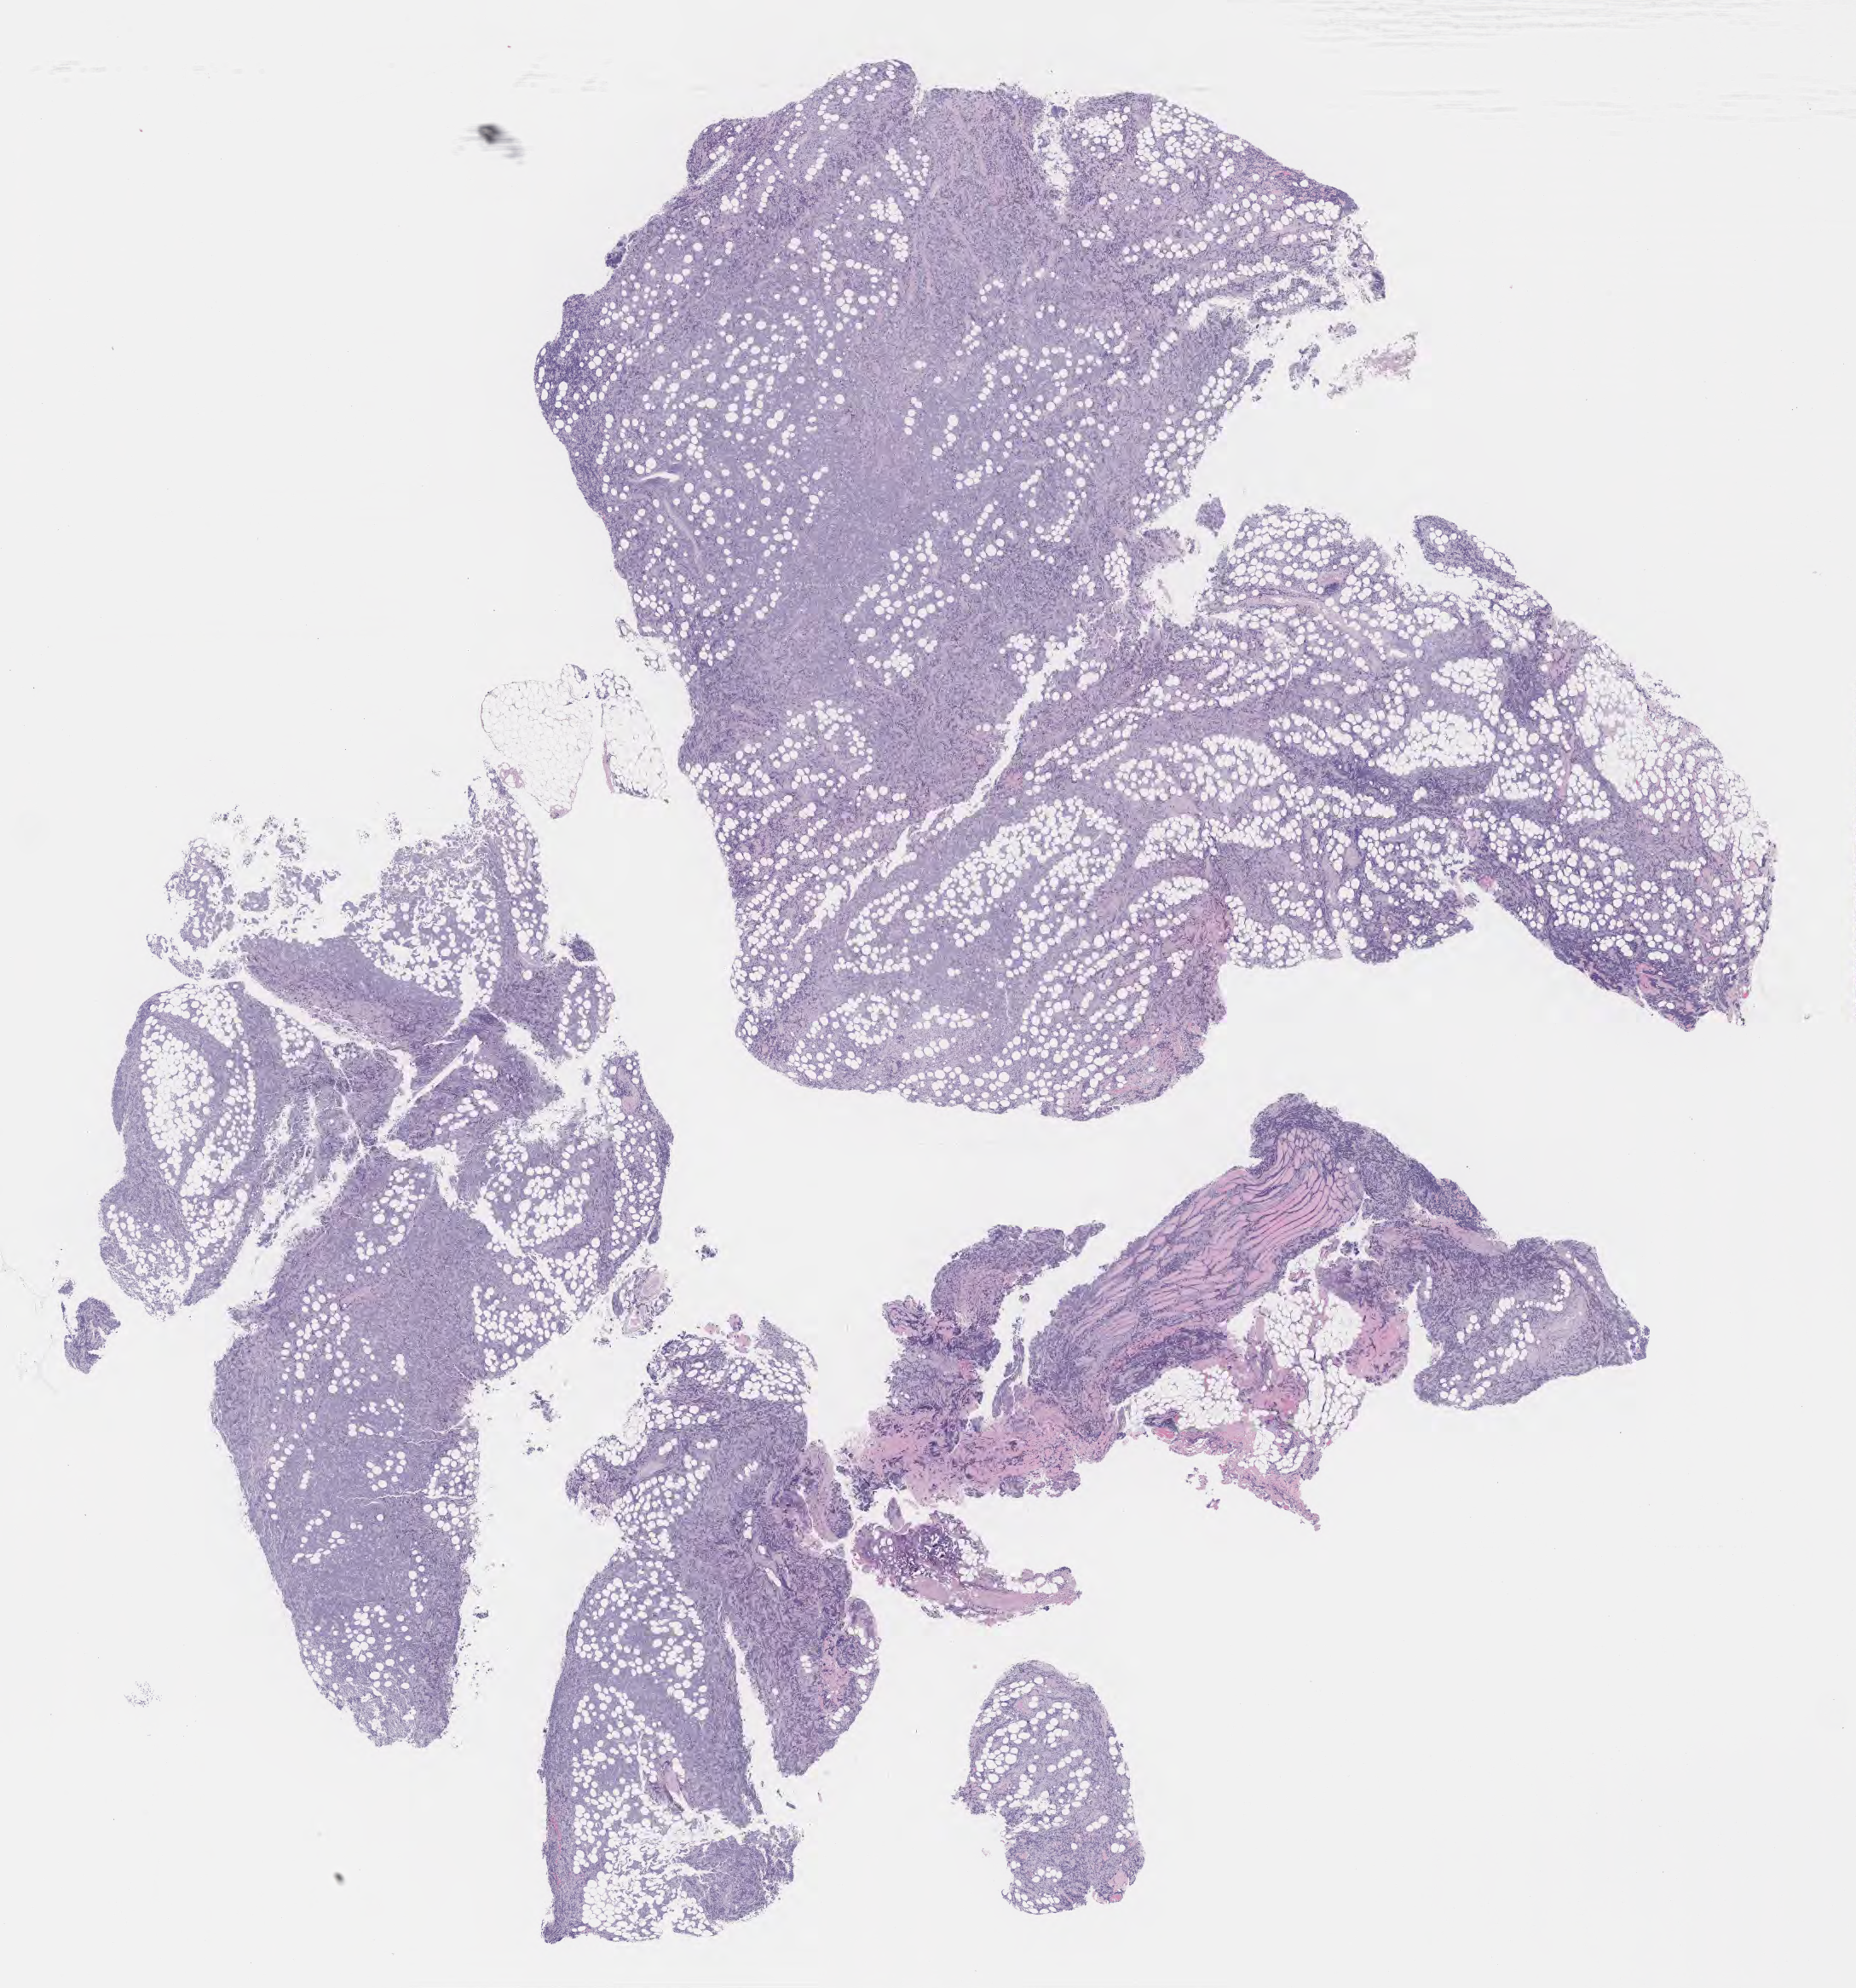
Whole-slide image, H&E stain — a low-resolution overview of the entire scanned area, about 17.6 x 18.9 mm, specimen: tumor tissue, anatomic site: lymph node of head and neck. Patient: male, aged 66.
Diagnosis: Burkitt lymphoma, NOS.